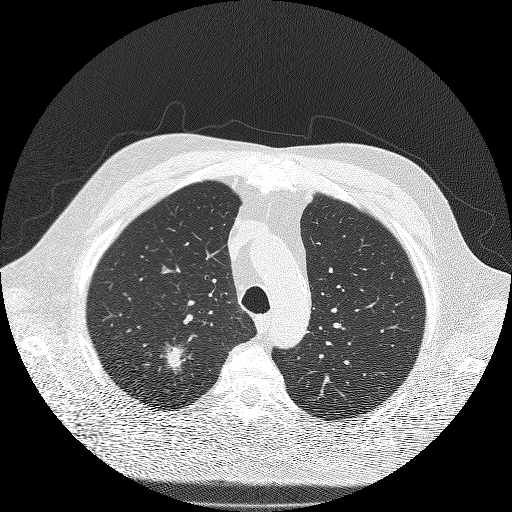
Low-dose screening chest CT, one axial slice; position 148 of 180 along the scan axis; lung window (W 1500 / L -600 HU); 2 mm slice thickness; 512 × 512 image matrix, field of view 385 × 385 mm.
Structures marked on this image (manually delineated by an expert):
- lesion 1 (tumor, upper lobe of right lung): bounding box [x1, y1, x2, y2] px = [161, 345, 186, 373]